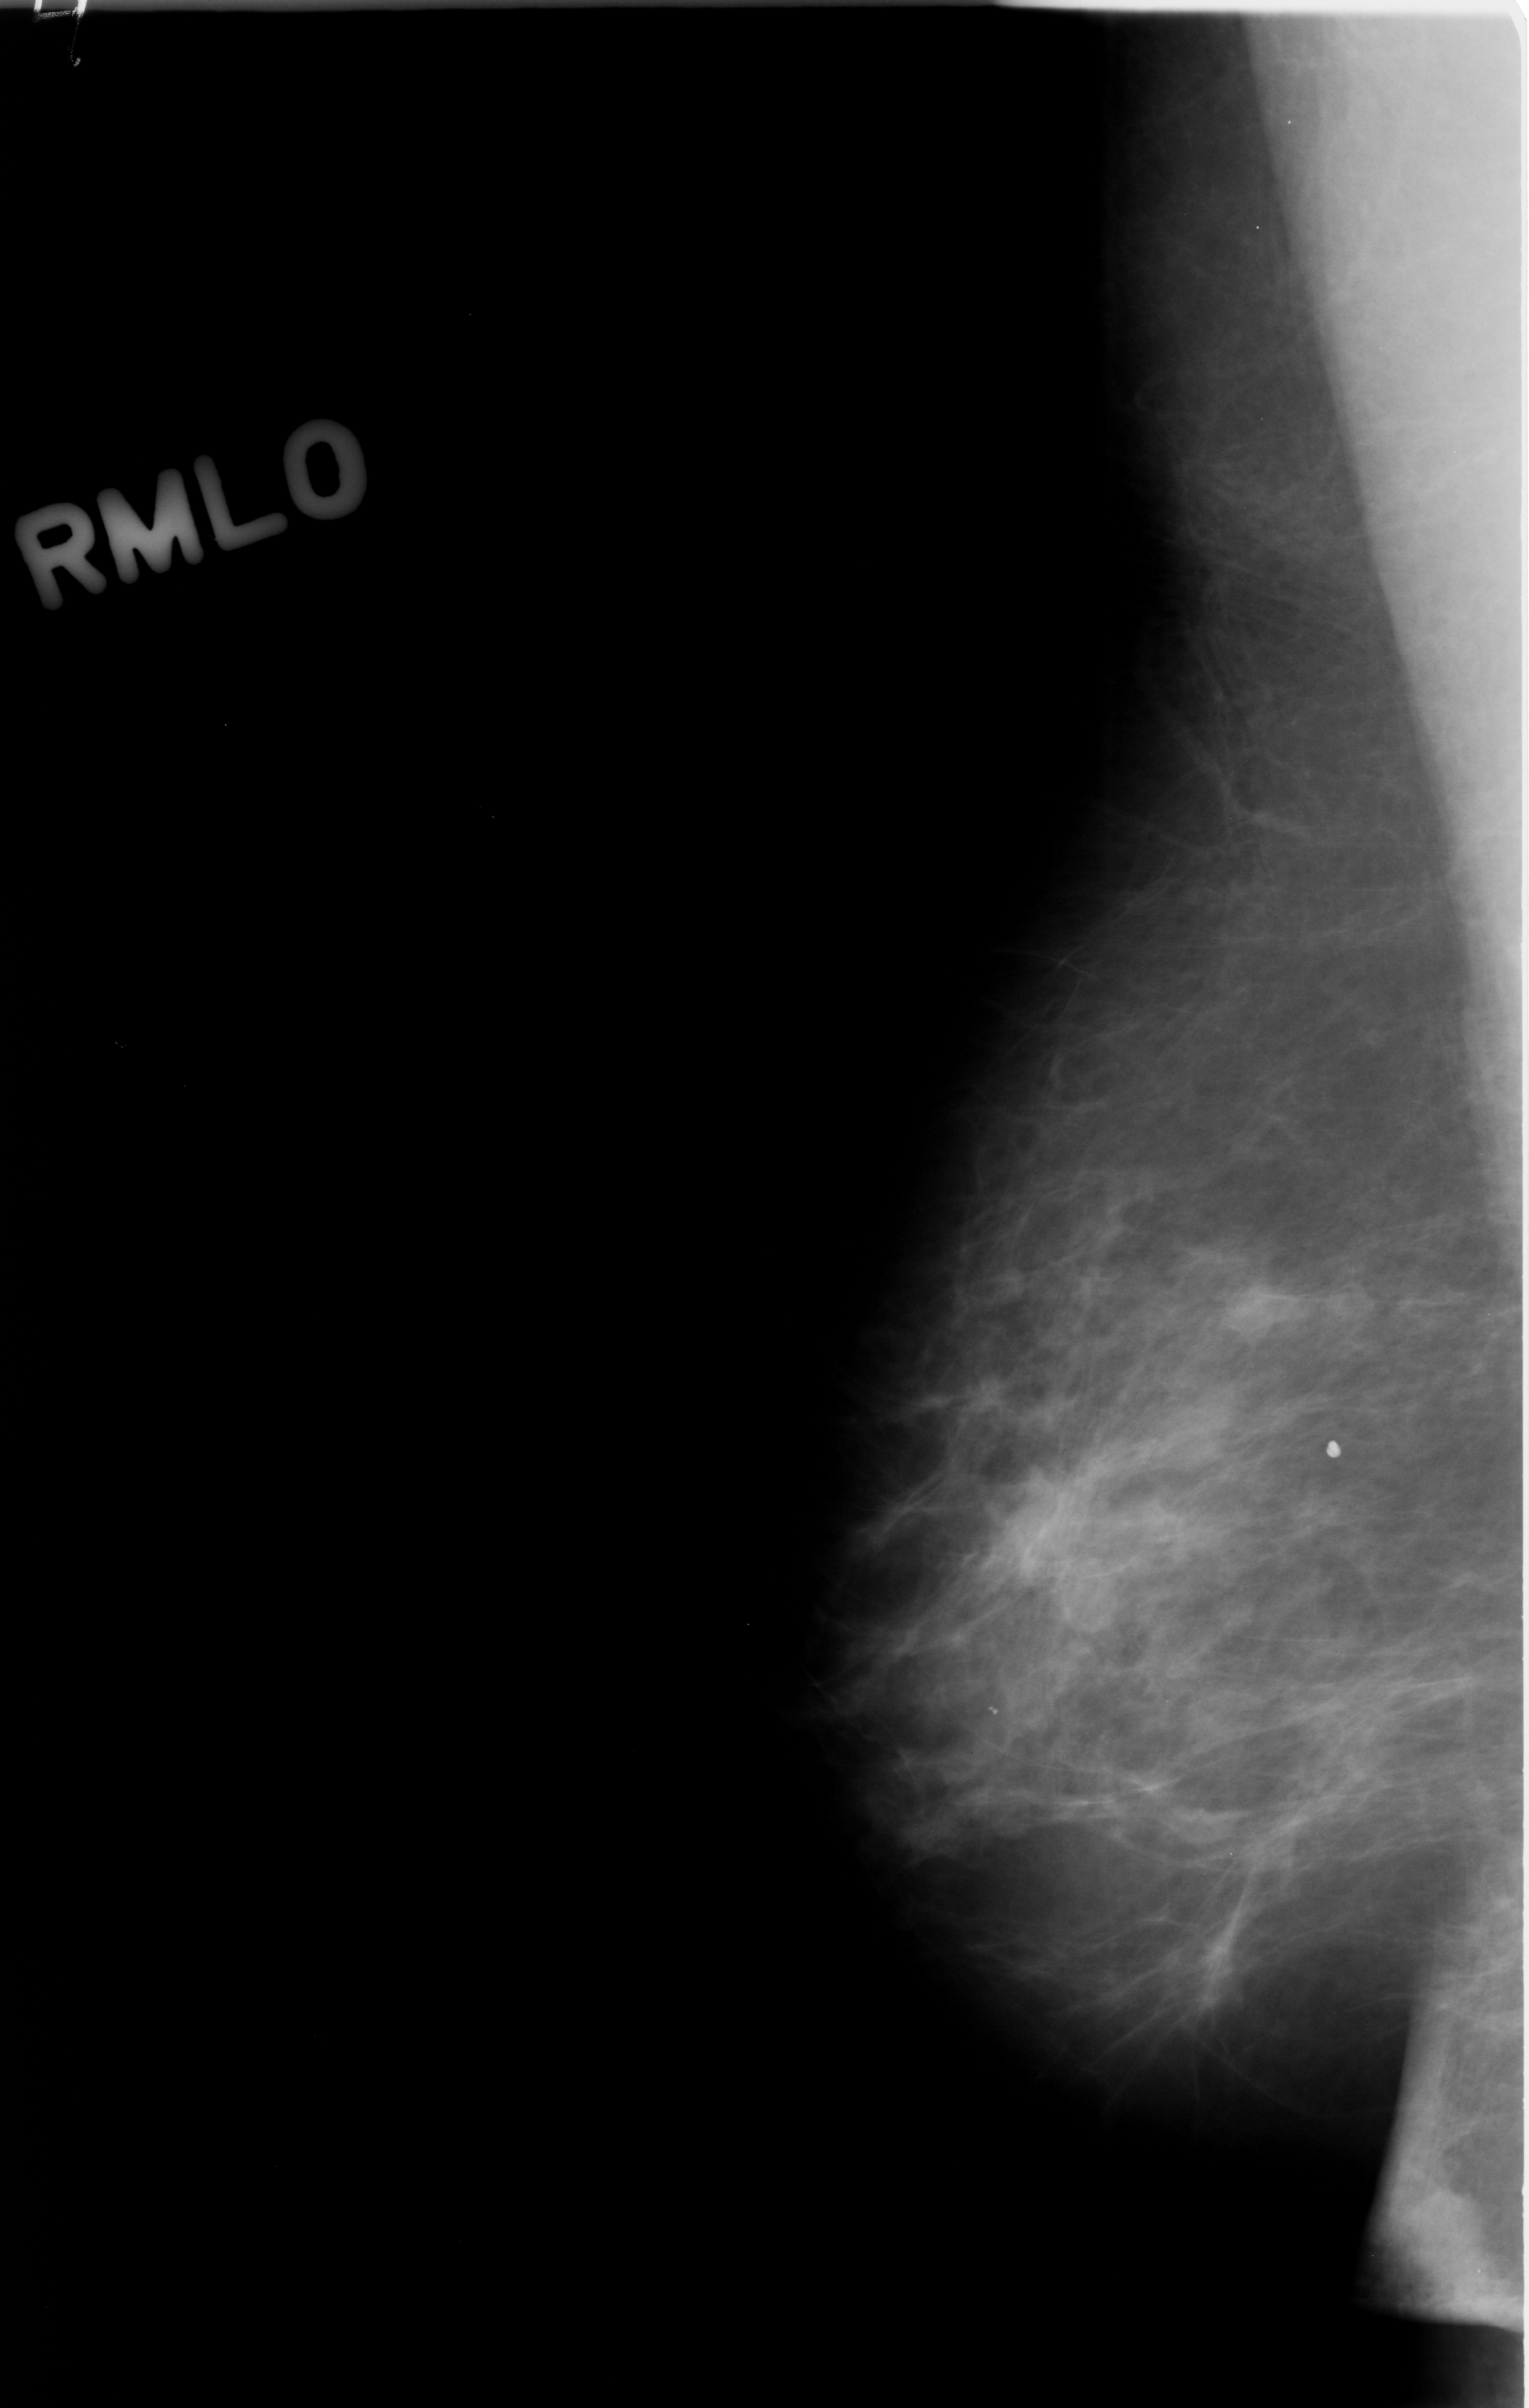
Digitized screen-film mammogram; right breast; MLO view; BI-RADS breast density category 2 (scale 1–4).
- Abnormality record for this image: mass, shape oval, margins circumscribed; BI-RADS assessment category 3; subtlety rating 4 on a 1 (subtle) to 5 (obvious) scale; benign without callback (not worked up further).